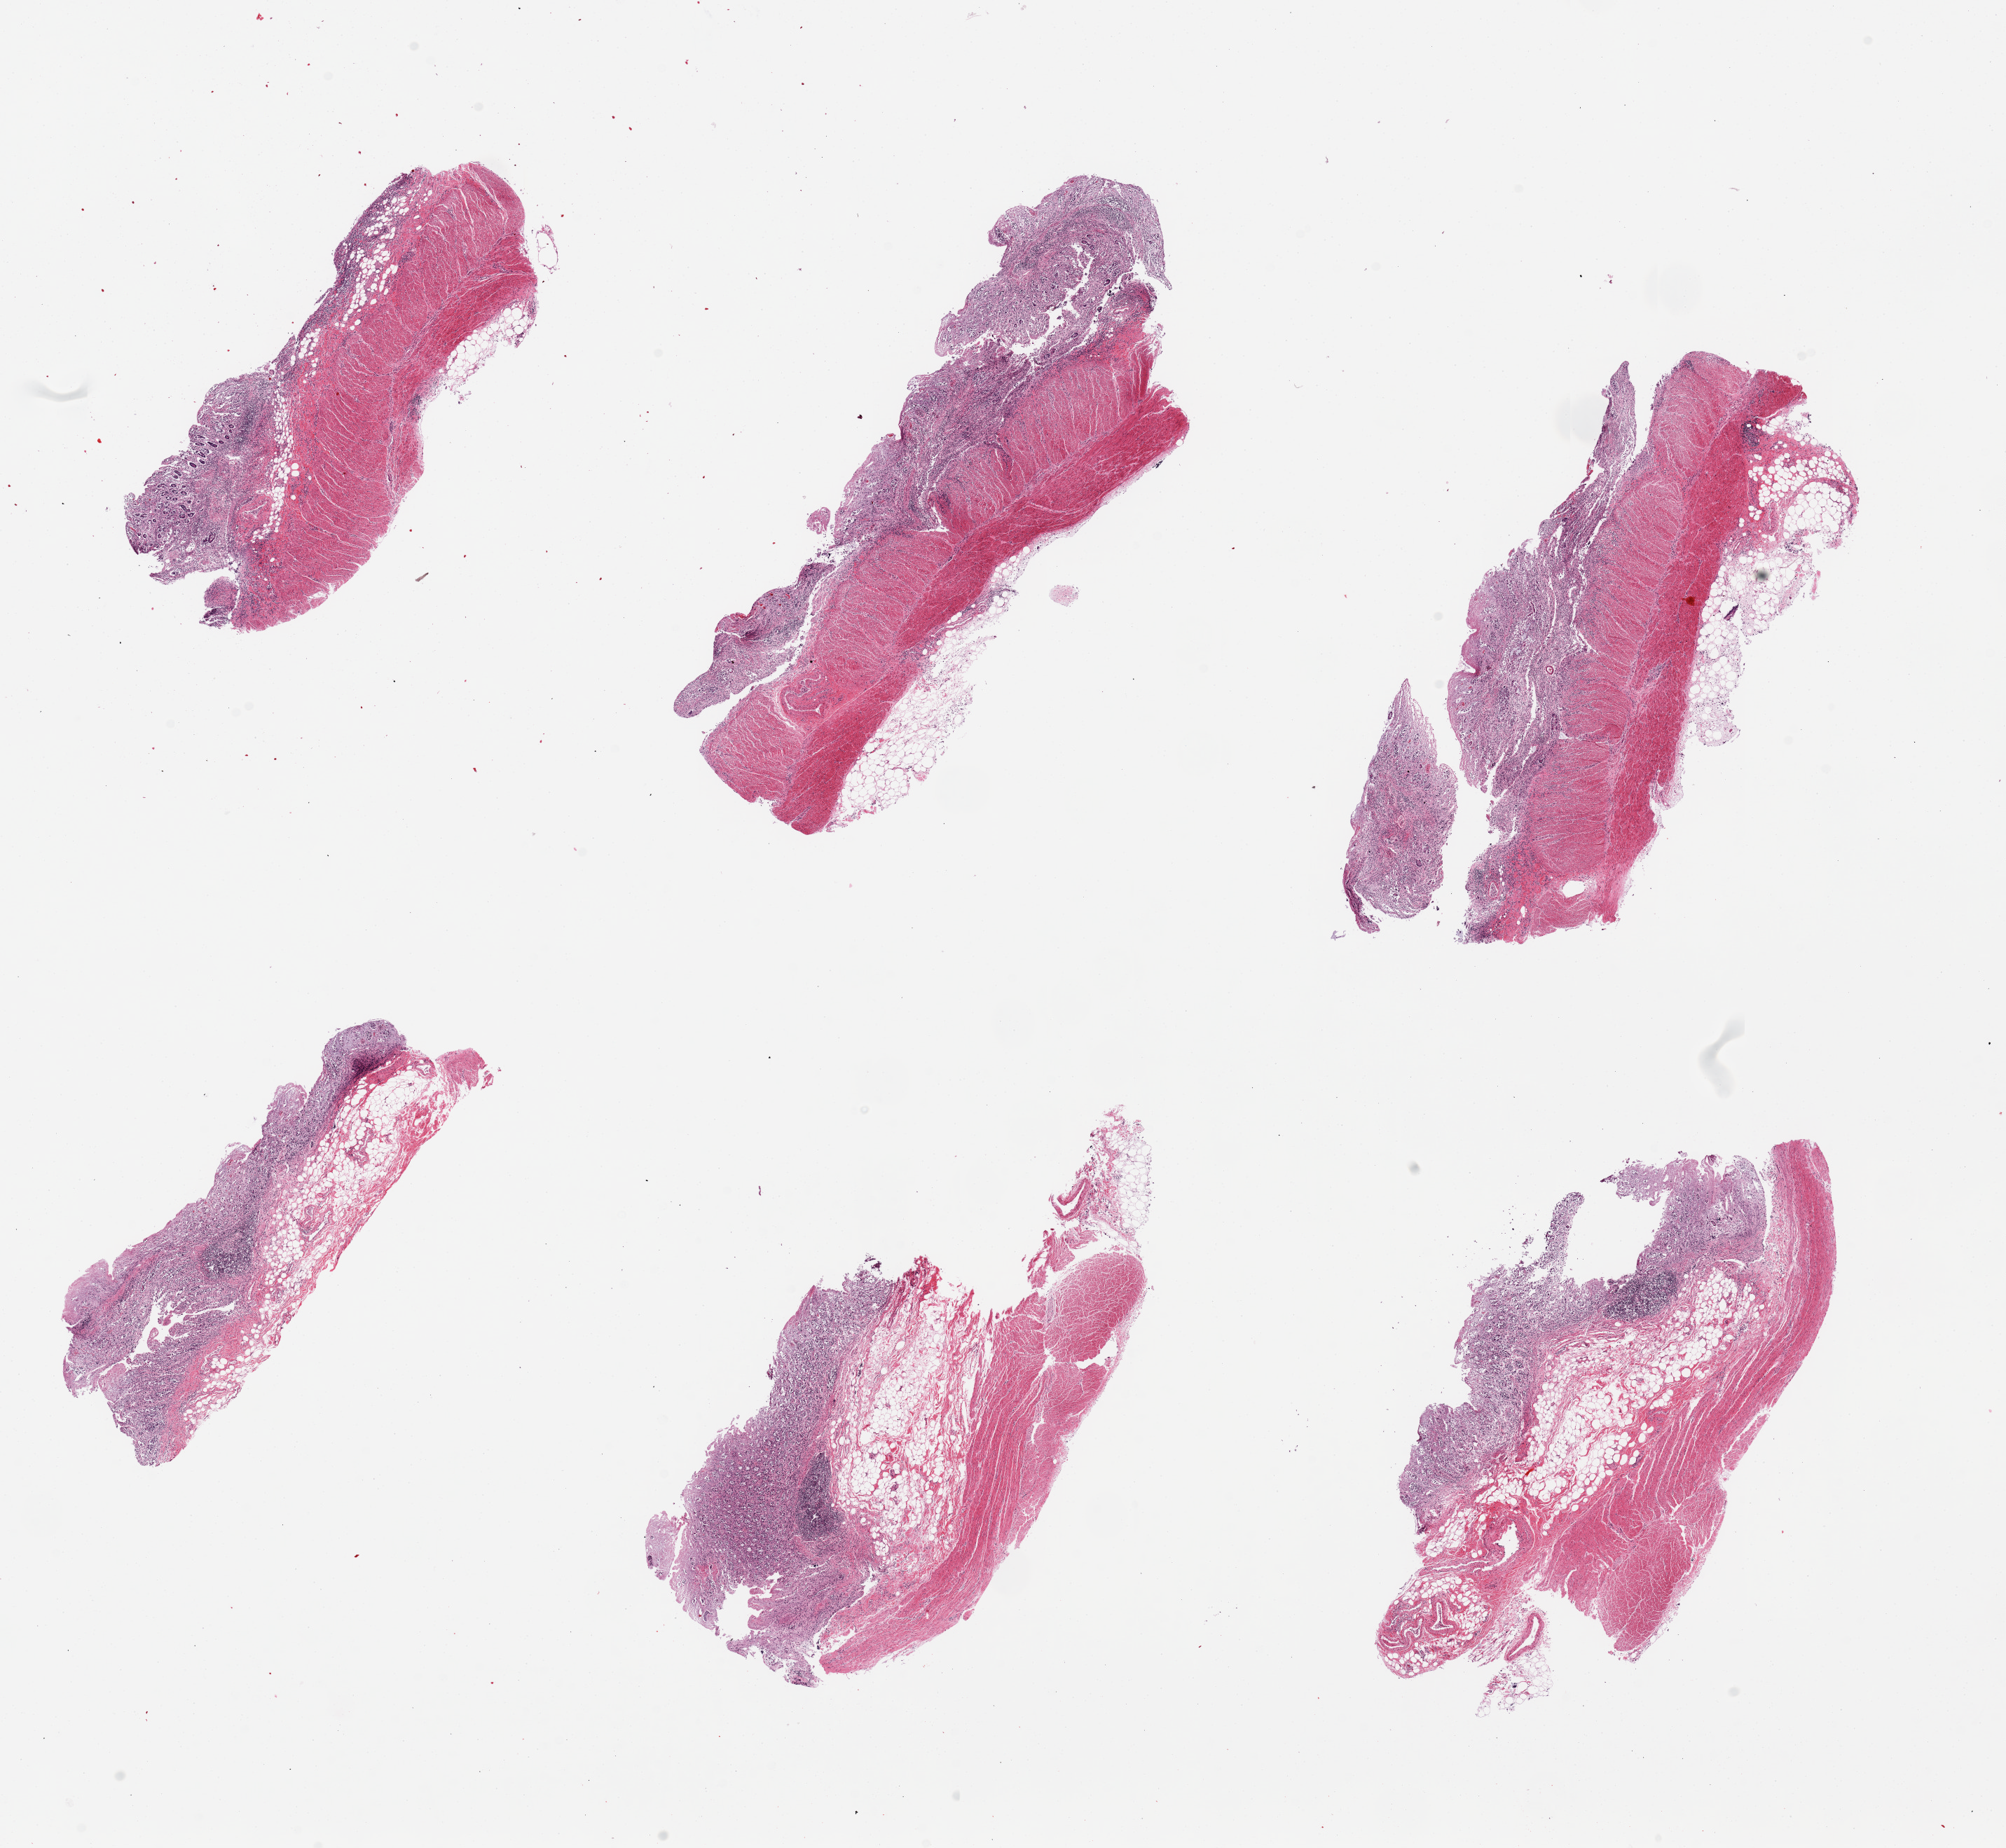
Whole-slide image, haematoxylin and eosin stain, a low-resolution overview of the entire scanned area, about 22.6 x 20.9 mm. PAXgene-fixed, paraffin-embedded tissue. Target tissue: transverse colon. Donor tissue sample. Donor sex: male.
Reviewer comment on this tissue sample: 6 pieces; mucosa severely autolyzed; muscularis preserved (1); chronicly inflamed mucosa consistent with history of ulcerative colitis.